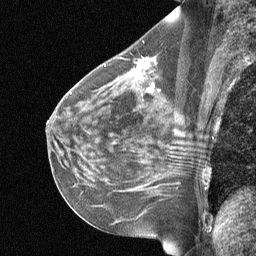
Breast MRI (dynamic contrast-enhanced), one sagittal slice. Slice 35 of 64 in the series (ordered by position). Dynamic contrast-enhanced study with each time point stored as its own series, time point 2 of 3 at this slice position (early post-contrast, ordered by acquisition time). 1.5 T. TE 4.8 ms, TR 27 ms. 2 mm slice thickness. 256 × 256 image matrix, field of view 200 × 200 mm. Patient: female, 51 years. From the clinical record (not read from this slice): setting: breast cancer imaged before/during neoadjuvant chemotherapy; receptor status: HR-positive, HER2-negative.
Outlined on this slice (semi-automatic segmentation, software-assisted and operator-edited):
- analysis volume of interest (the breast-tissue region the enhancement analysis was run in; not a lesion): bounding box [x1, y1, x2, y2] px = [88, 42, 190, 119]
- tumour enhancement mask (voxels above the 90 % enhancement threshold inside the analysis volume of interest): [132, 58, 153, 92]